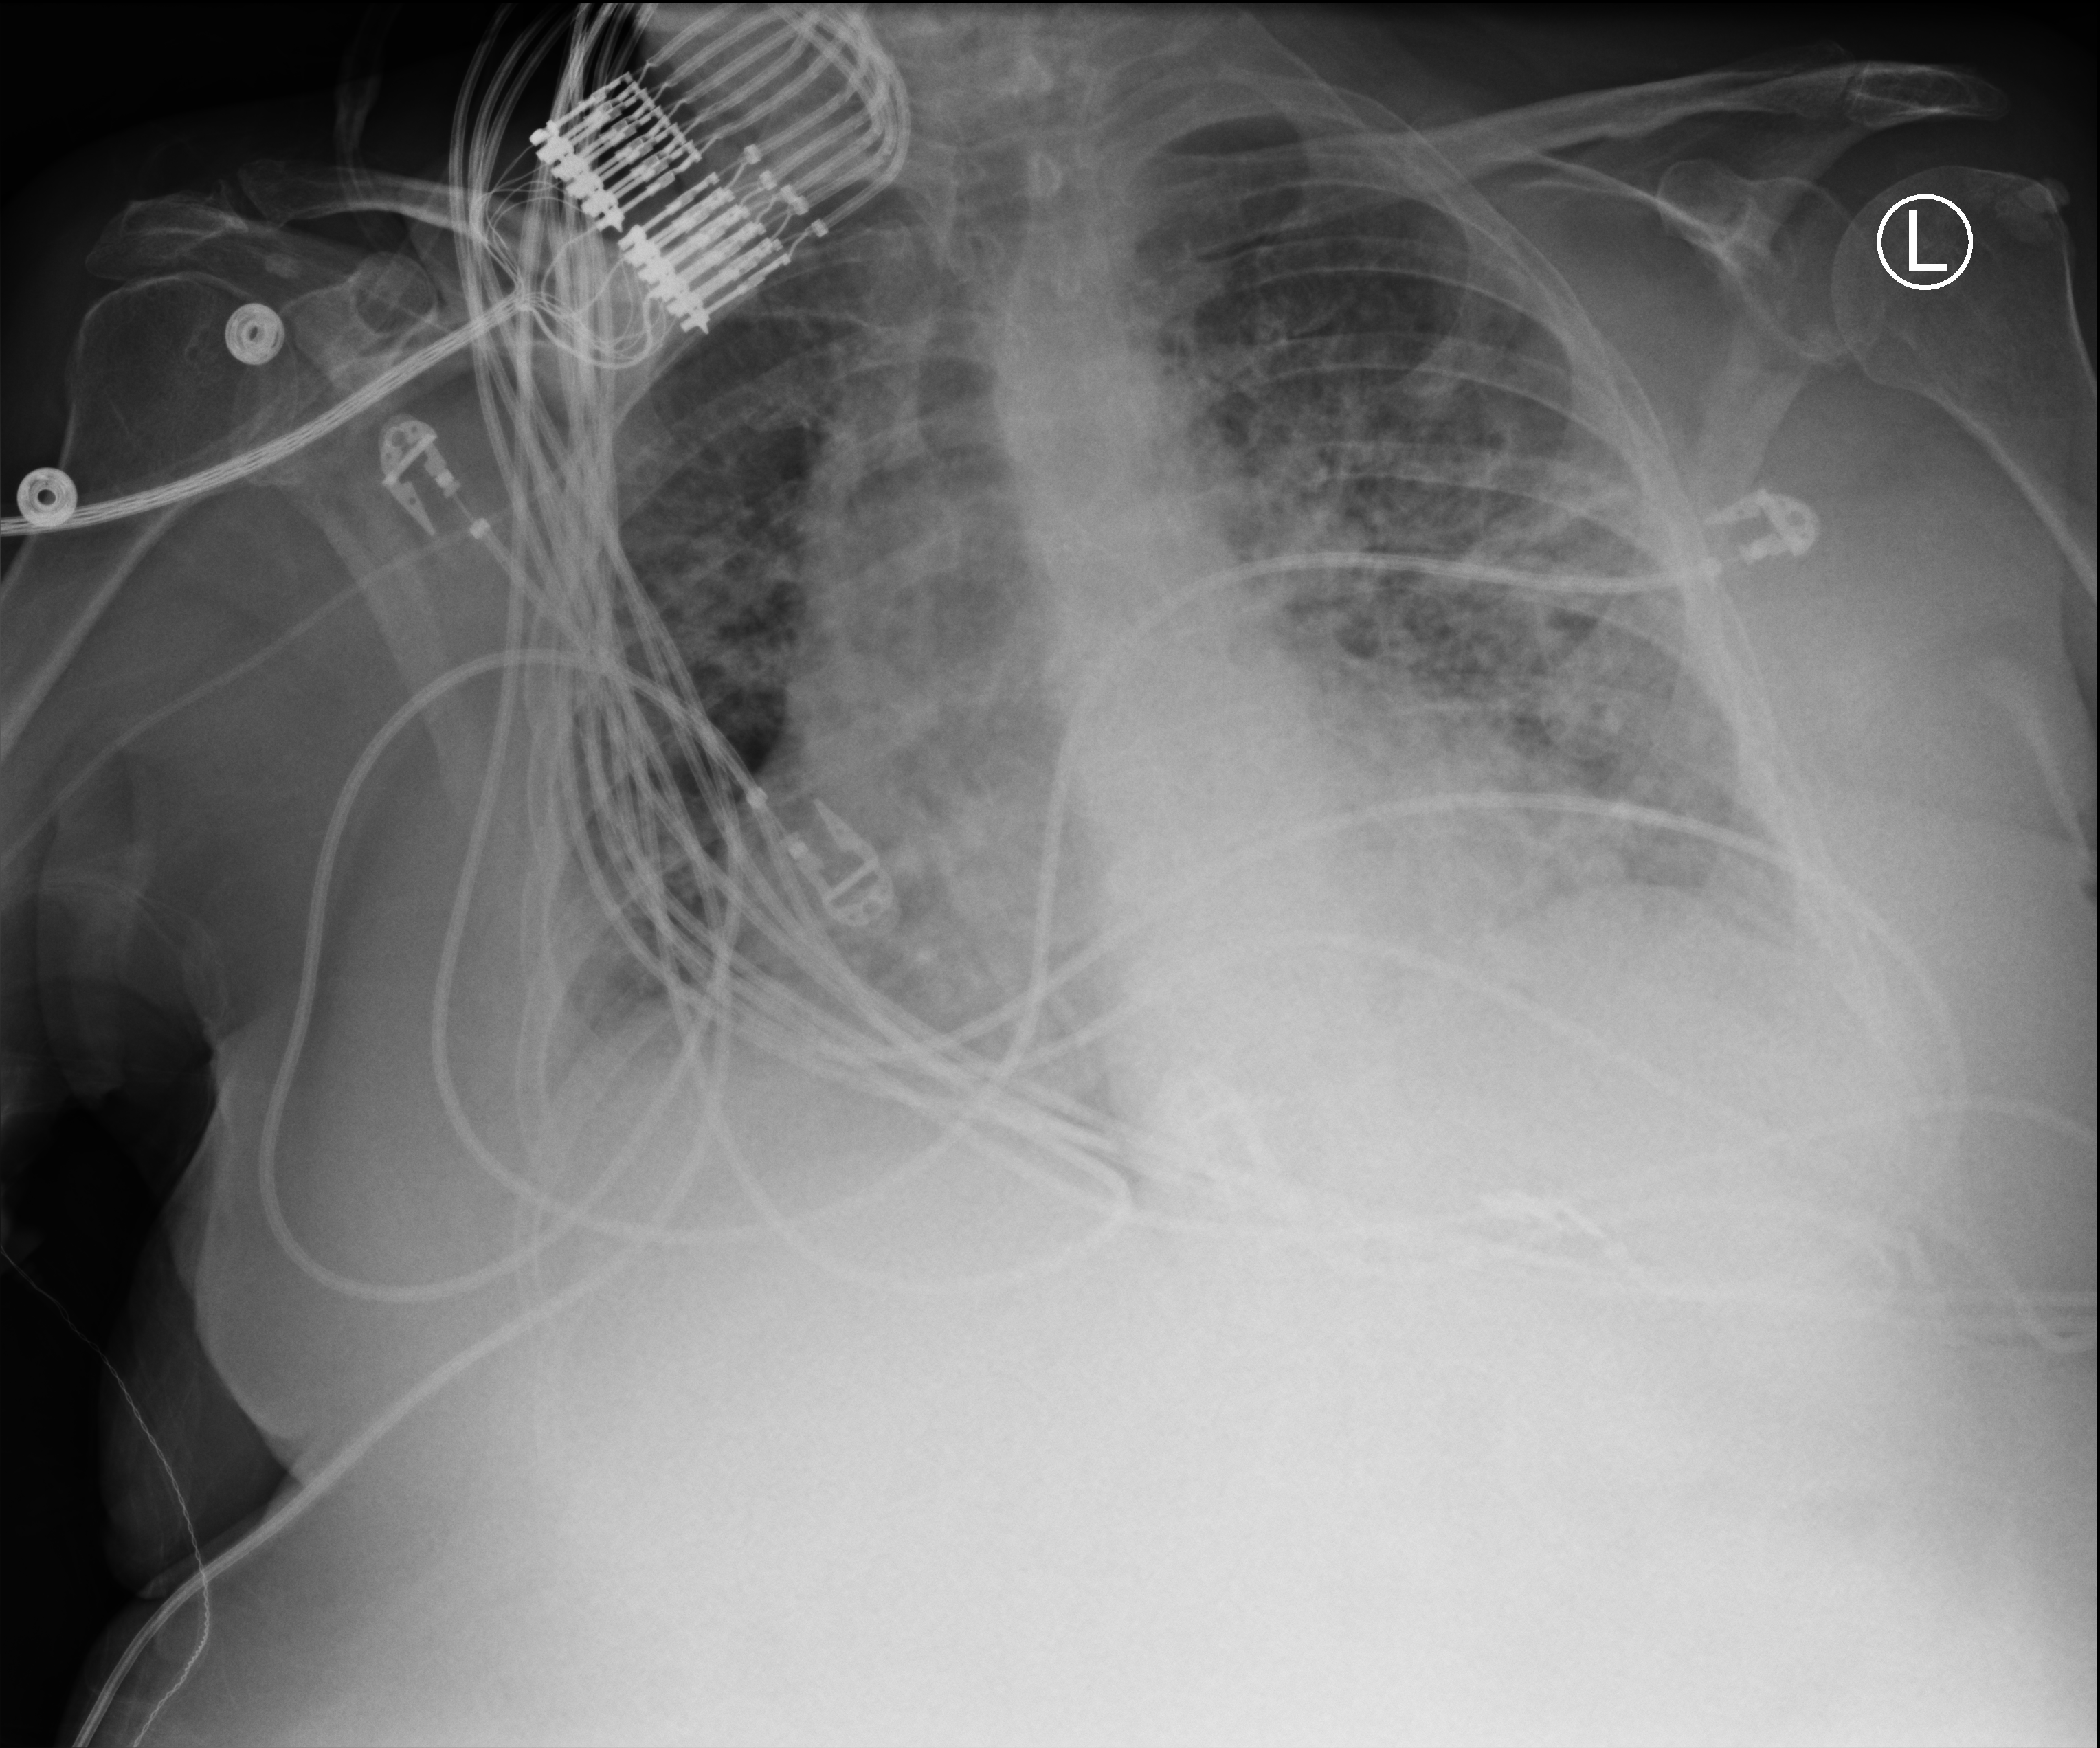
Chest X-ray (portable). Patient hospitalised with COVID-19; female, aged 75–90 years.
From the hospital-stay record, not from the radiograph (when in the stay this image was taken is not recorded):
- admitted to intensive care during this hospital stay: yes
- mechanically ventilated during this hospital stay: yes
- chronic kidney disease (admission record): no